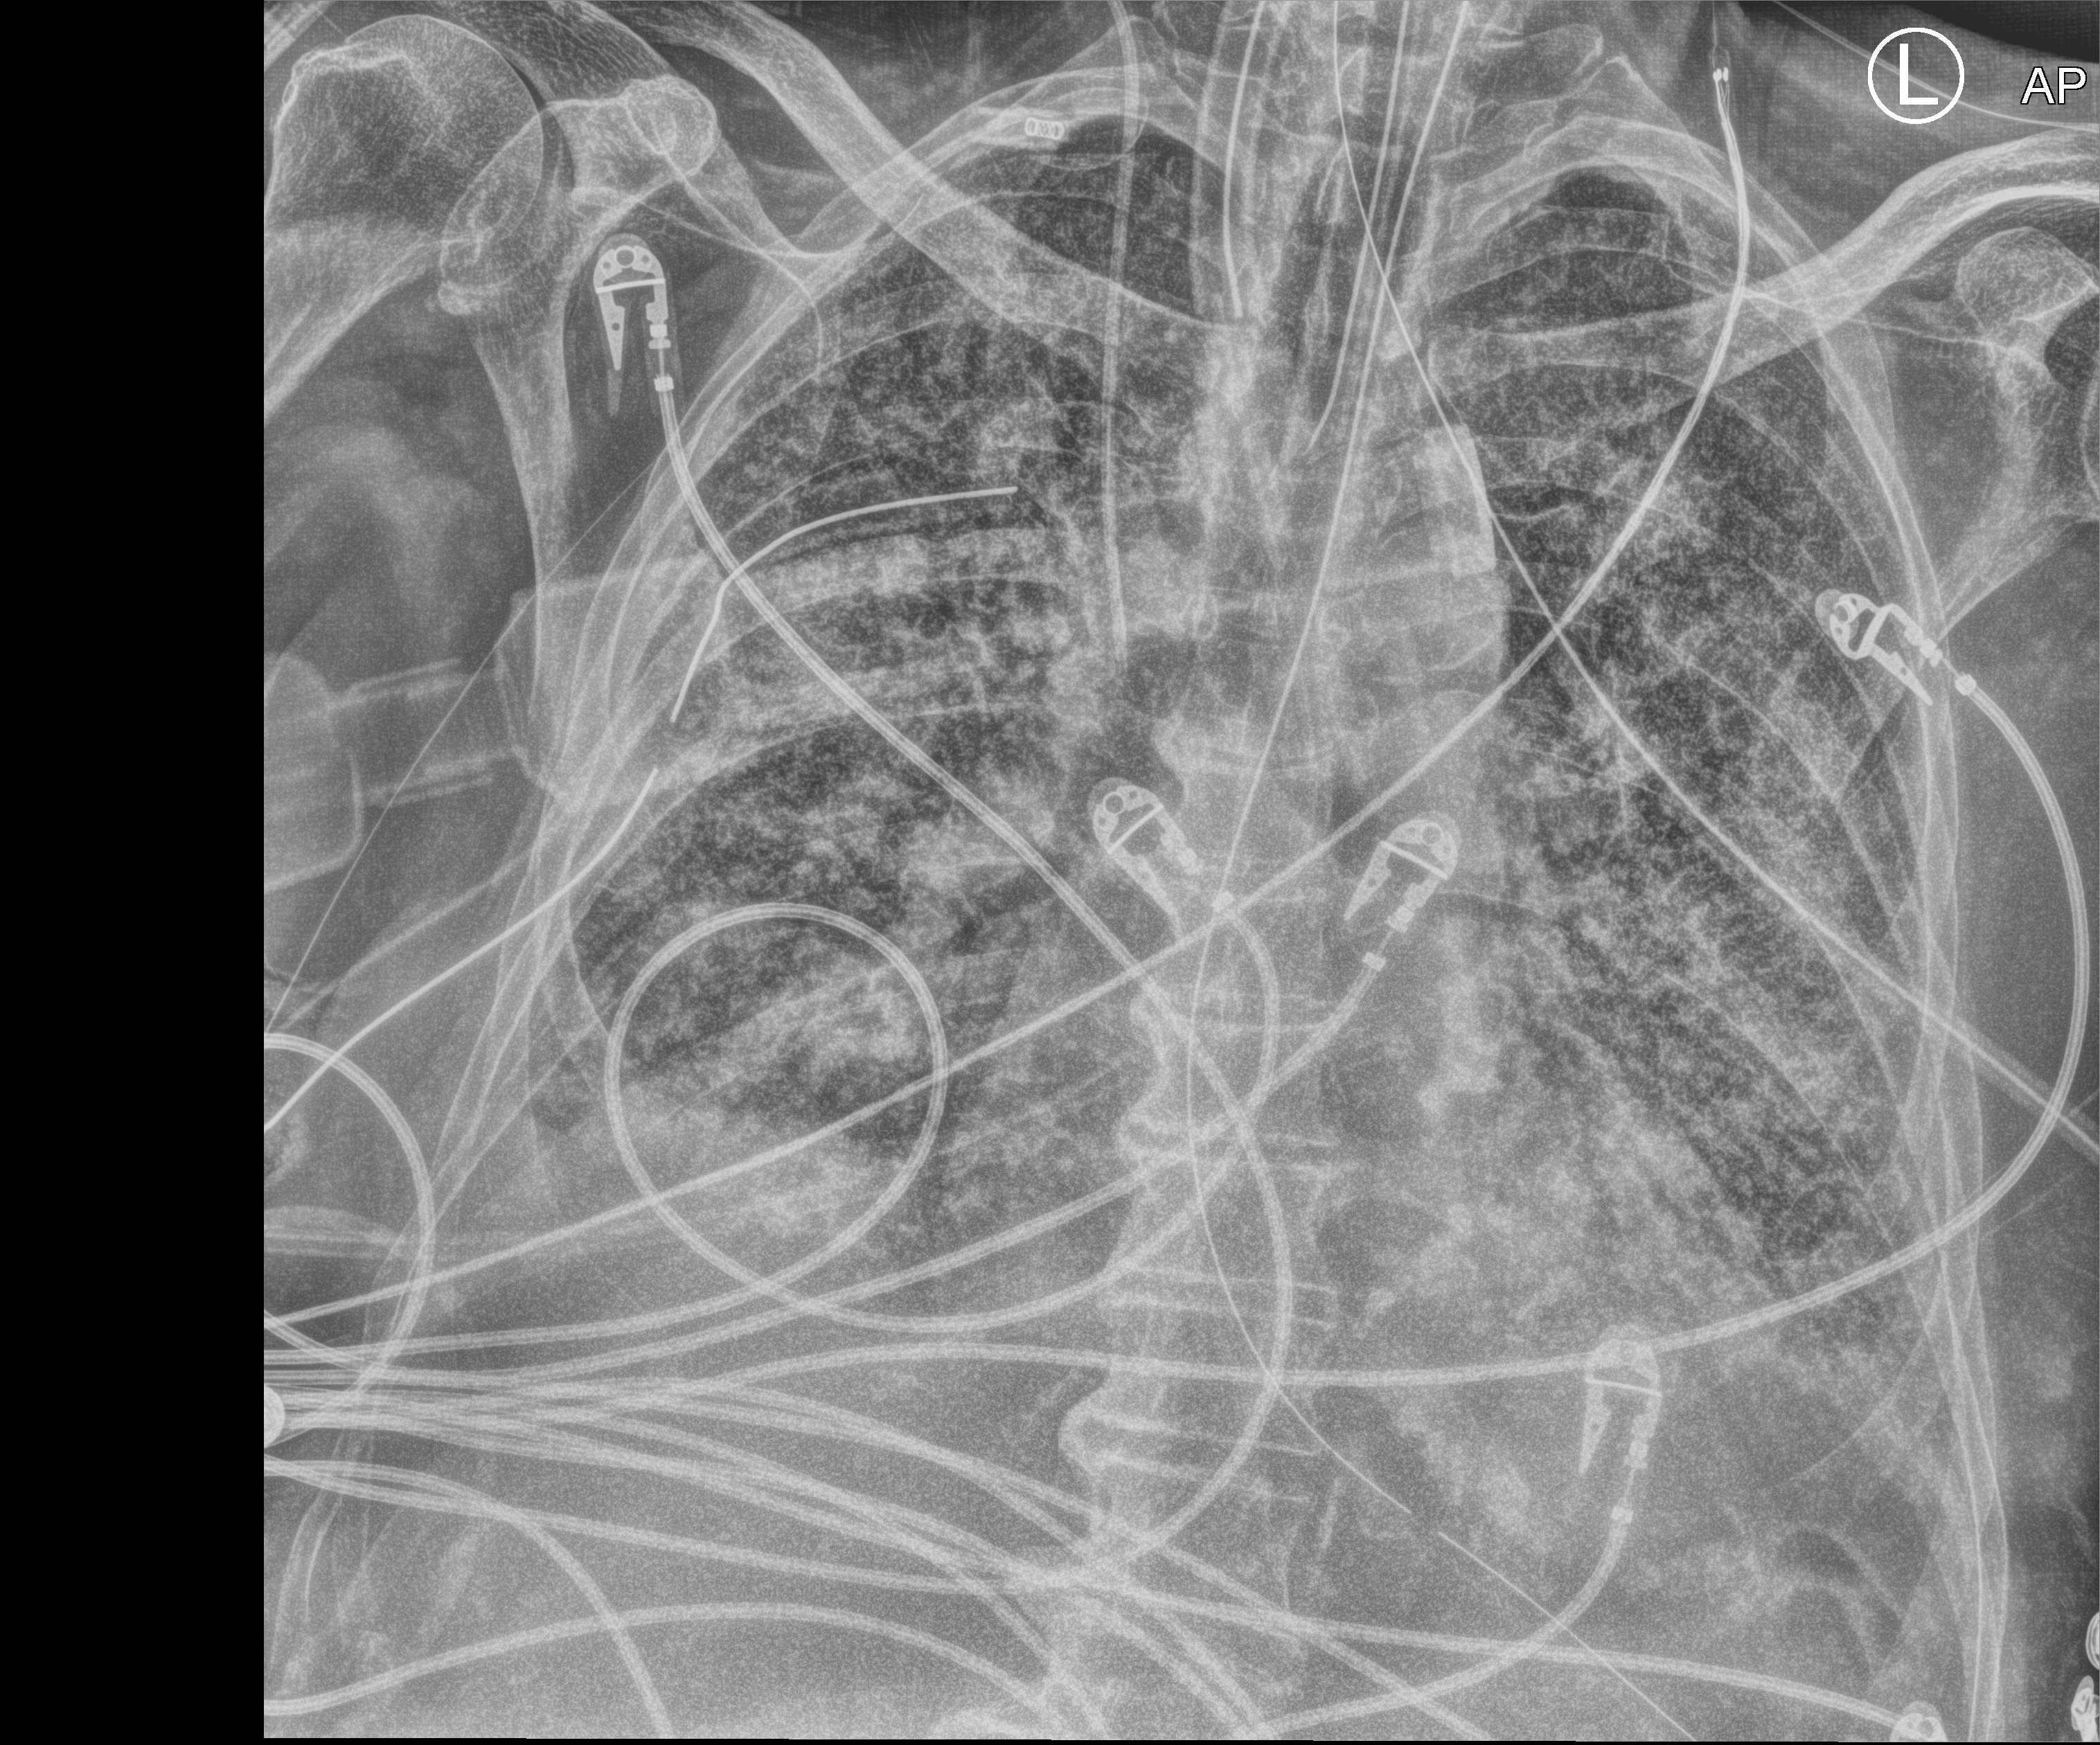
Chest X-ray (portable); anteroposterior (AP) projection. Patient hospitalised with COVID-19; male, aged 75–90 years.
Admission-level facts for this patient (not findings on this image; timing relative to this image not recorded): other chronic lung disease (admission record): no.